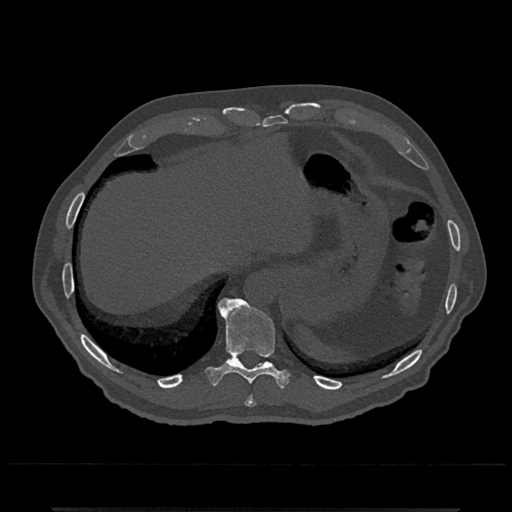
CT including the spine, one axial slice. Position 552 of 797 along the scan axis. 120 kVp. Bone window (W 1800 / L 400 HU). 0.5 mm slice thickness. 512 × 512 image matrix, field of view 393 × 393 mm. Patient: male, 67 years. From the clinical record (not read from this slice): primary cancer: prostate.
Annotated regions visible in this slice (semi-automatic segmentation, software-assisted and operator-edited):
- T10 vertebra: box from (x=206, y=297) to (x=289, y=388) px
- T11 vertebra: (x=229, y=357)–(x=238, y=360)
- T9 vertebra: (x=245, y=396)–(x=256, y=407)